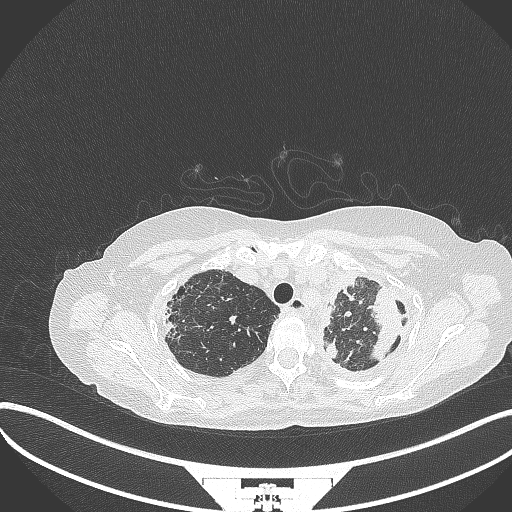
Chest CT, one axial slice; slice 284 of 373 in the series (ordered by position); lung window (W 1500 / L -600 HU); 1 mm slice thickness; 512 × 512 image matrix, field of view 400 × 400 mm. Patient: female, 56 years. From the clinical record (not read from this slice): clinical TNM (as recorded): T1 N0 M0.
Outlined on this slice (bounding box drawn by a radiologist):
- lung tumour (recorded histology: adenocarcinoma): bounding box (x1, y1, x2, y2) in pixels: (365, 284, 406, 370)